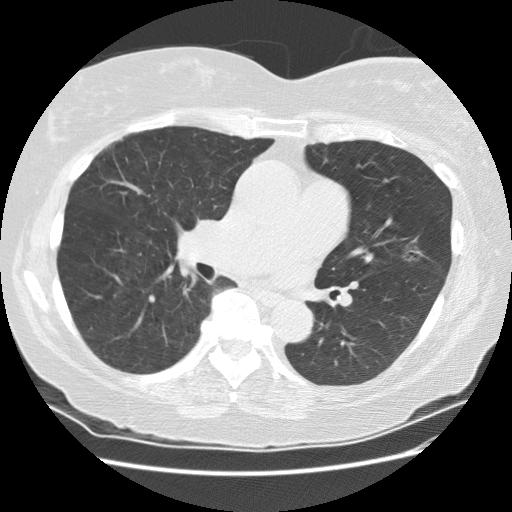
Low-dose screening chest CT, one axial slice. Slice 98 of 180 in the series (ordered by position). Reconstruction kernel STANDARD. Lung window (W 1500 / L -600 HU). 512 × 512 image matrix.
Structures marked on this image (outlined manually by an expert reader):
- lesion 1 (tumor, upper lobe of left lung): bounding box [x1, y1, x2, y2] px = [404, 245, 423, 262]